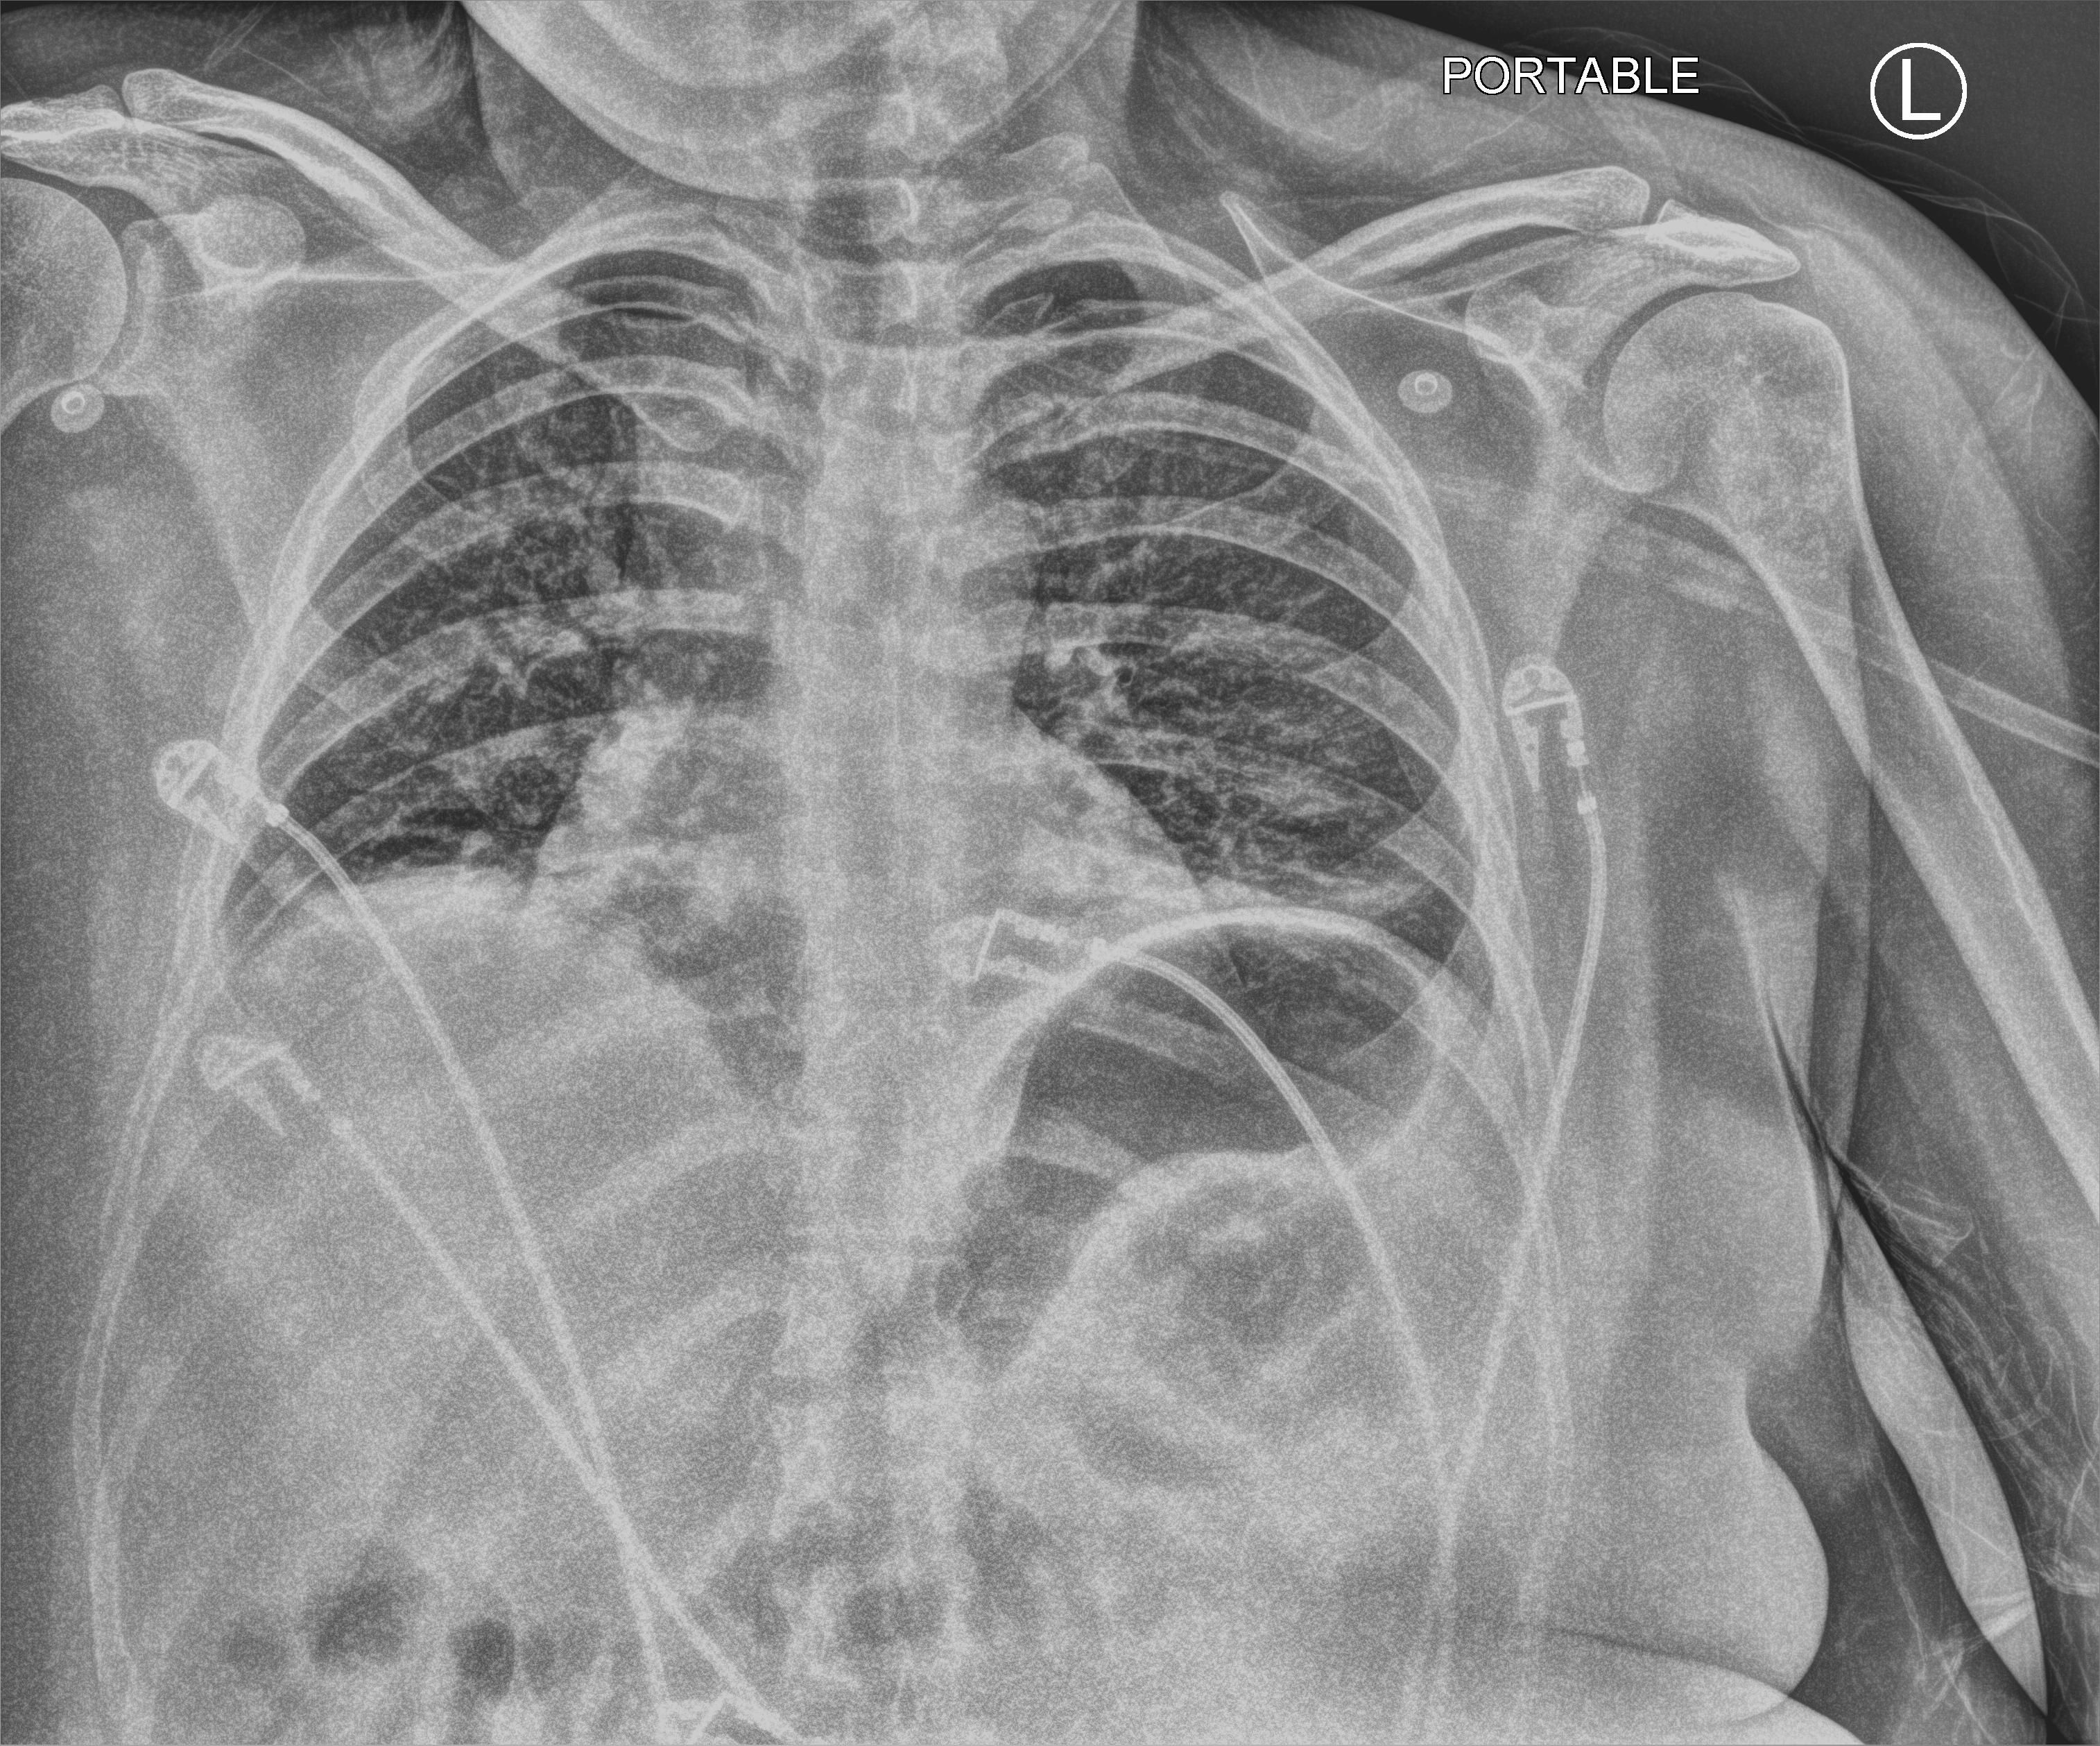
Chest X-ray (portable), anteroposterior (AP) projection. Female patient hospitalised with COVID-19, age 18–59 years.
Hospital-stay facts (about this admission, not read from this image; timing relative to this image not recorded):
- mechanically ventilated during this hospital stay: no
- hypertension (admission record): no
- COPD (admission record): no